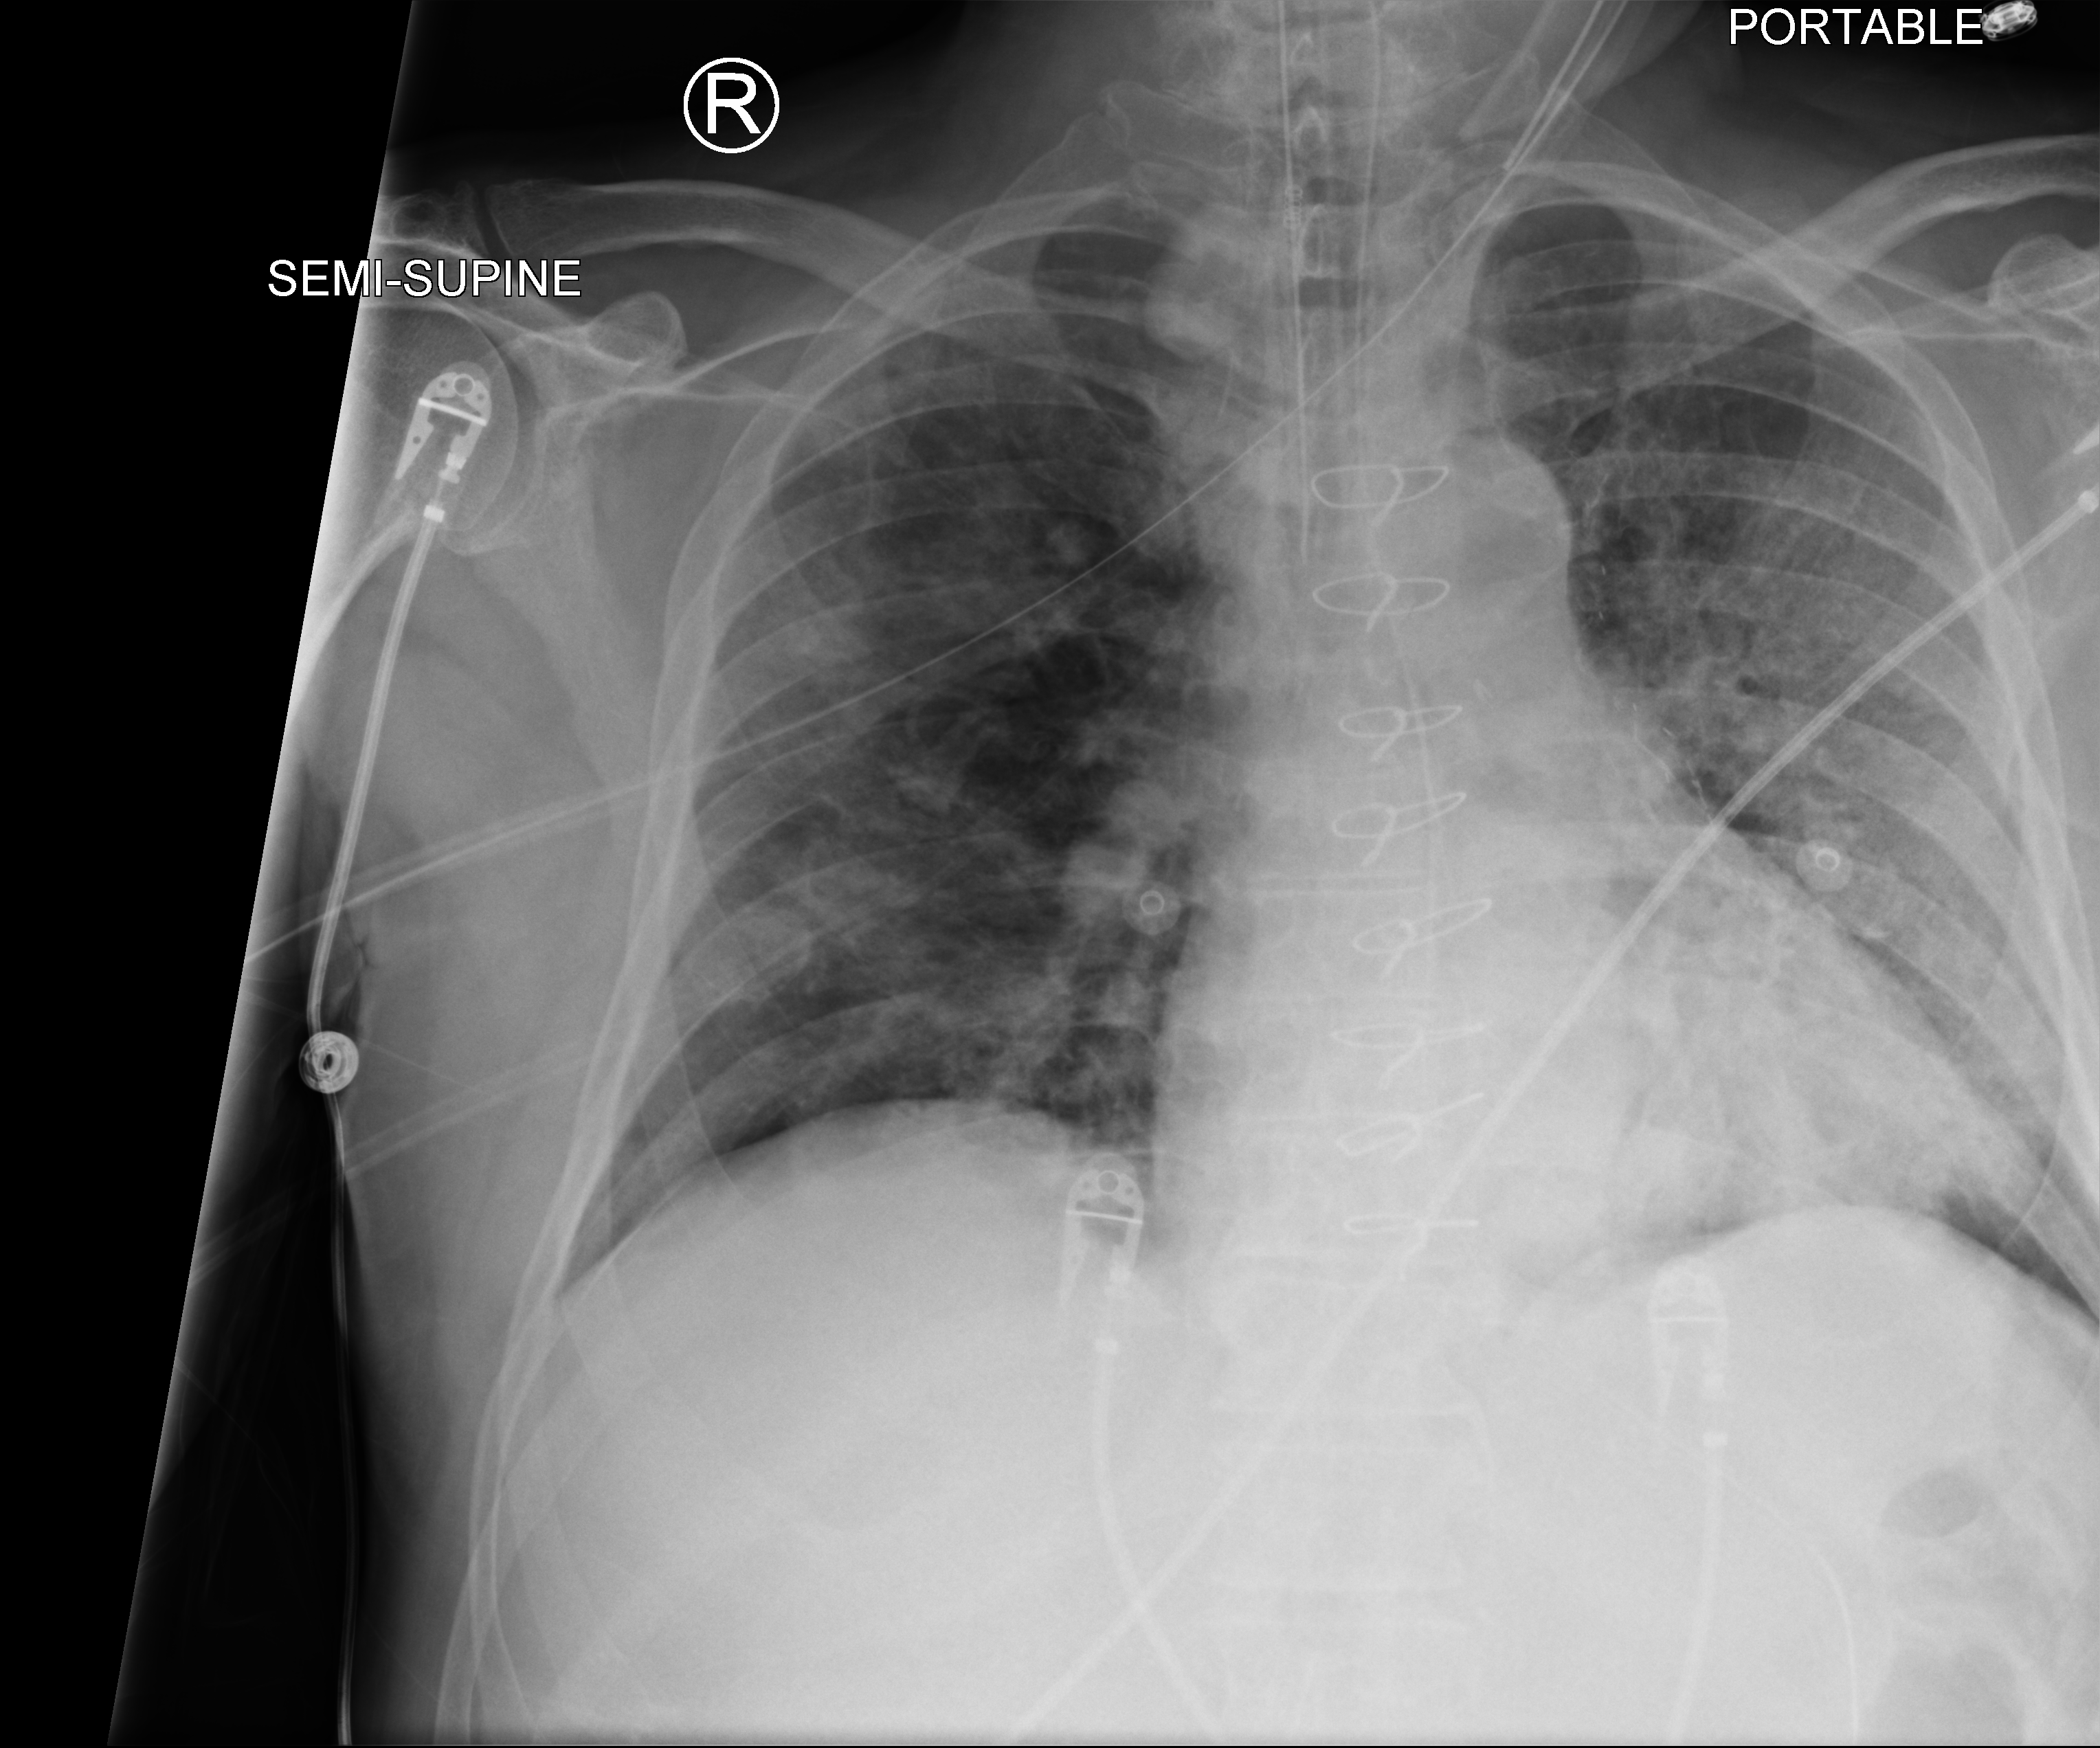
Bedside chest radiograph (computed radiography); anteroposterior (AP) projection. Patient hospitalised with COVID-19; male, aged 60–74 years.
Admission-level facts for this patient (not findings on this image; timing relative to this image not recorded):
- admitted to intensive care during this hospital stay: yes